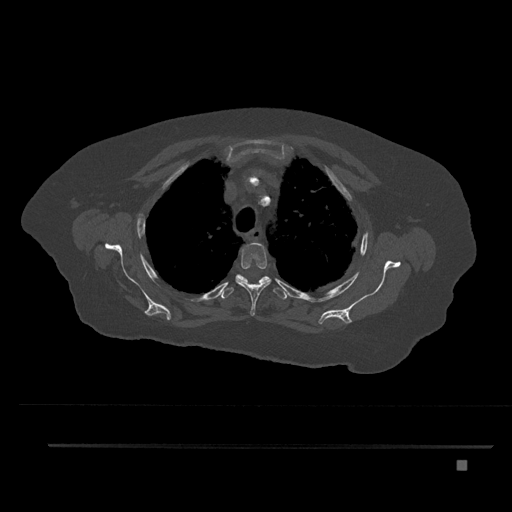
CT including the spine, one axial slice. Position 627 of 797 along the scan axis. Bone window (W 1800 / L 400 HU). 0.5 mm slice thickness. 512 × 512 image matrix, field of view 437 × 437 mm. Female patient, age 76 years. Case-level facts recorded for this patient, not image findings: primary cancer: lung; vertebrae with lytic lesions (as recorded): T11, L3.
Outlined on this slice (semi-automatic segmentation, software-assisted and operator-edited):
- T3 vertebra: bounding box (x1, y1, x2, y2) in pixels: (235, 242, 271, 316)
- T4 vertebra: (220, 274, 287, 300)